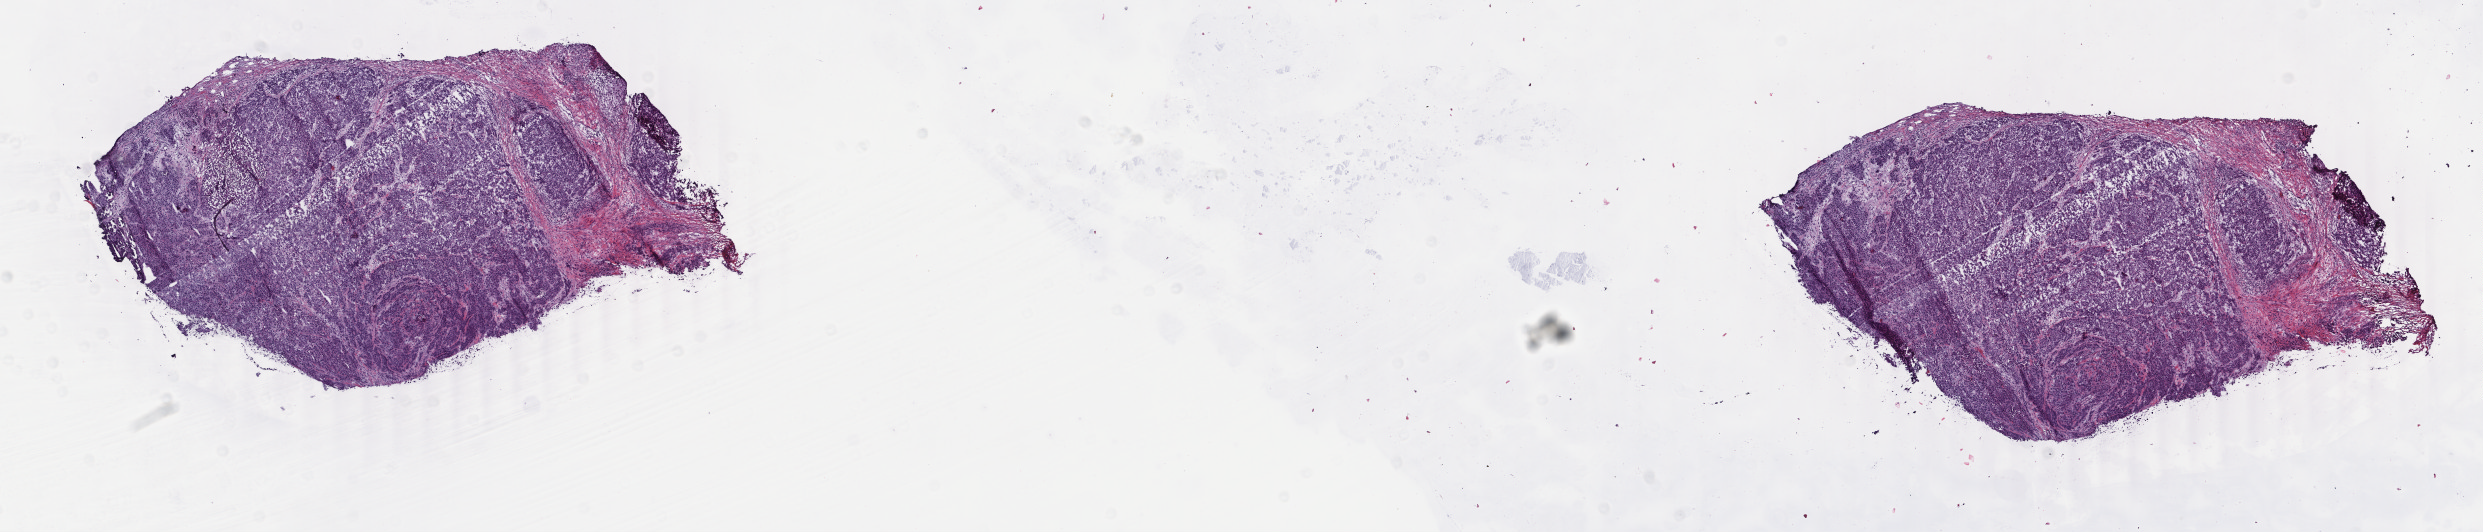
Whole-slide histology image, H&E-stained, shown as a low-resolution overview of the whole scanned area (about 19.8 x 4.2 mm, from a 40x scan); frozen section from the top of the tissue portion; sample: primary tumour, breast. Female, age 69 years at initial diagnosis. Pathologist review of this section (percent, as recorded): tumour cells 80%, tumour nuclei 80%, normal cells 0%, stromal cells 20%, necrosis 0%. Inflammatory infiltration, as recorded: lymphocyte infiltration 7%, monocyte infiltration 3%, neutrophil infiltration 1%.
* laterality: right
* AJCC pathologic stage: IIA
* diagnosis: Infiltrating duct carcinoma, NOS